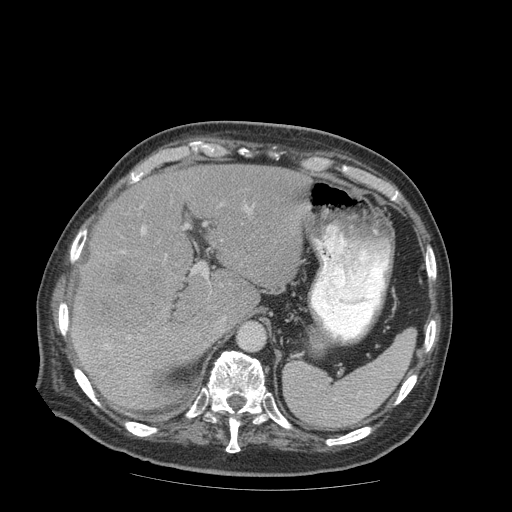
Contrast-enhanced abdominal CT (liver protocol), one axial slice; position 59 of 99 along the scan axis; reconstruction kernel STANDARD; 140 kVp; soft-tissue window (W 400 / L 40 HU); 2.5 mm slice thickness; 512 × 512 image matrix. Case-level facts recorded for this patient, not image findings: diagnosis: hepatocellular carcinoma (patient treated with transarterial chemoembolisation; whether this scan precedes or follows treatment is not stated here); TNM stage (as recorded): Stage-IIIB; Child-Pugh class: A; tumour nodularity: multinodular.
Annotated regions visible in this slice (semi-automatically segmented with operator editing):
- liver parenchyma outside the tumour (the mass and vessels are separate outlines, so this box may not span the whole liver): bounding box [x1, y1, x2, y2] px = [70, 166, 309, 410]
- mass: [74, 243, 173, 336]
- liver vessels: [104, 205, 250, 349]